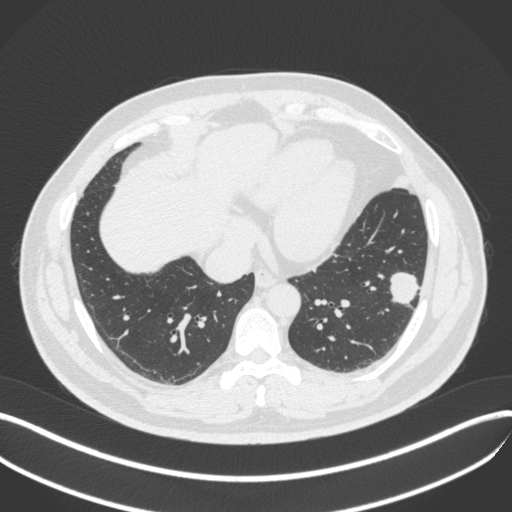
Chest CT, one axial slice; position 138 of 420 along the scan axis; lung window (W 1500 / L -600 HU); 1 mm slice thickness; 512 × 512 image matrix. Patient: male, 39 years. From the clinical record (not read from this slice): clinical TNM (as recorded): T2a N0 M0; histopathological grade: G2-3.
Structures marked on this image (rectangle marked by the reading radiologist):
- lung tumour (recorded histology: adenocarcinoma): bounding box (x1, y1, x2, y2) in pixels: (386, 267, 423, 306)